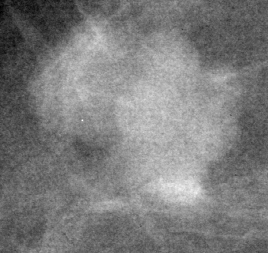
Crop from a digitized film mammogram around one marked abnormality; right breast; MLO view; BI-RADS breast density category 1 (scale 1–4).
Marked abnormality: mass, shape lobulated, margins circumscribed / ill defined; BI-RADS assessment category 4; pathology result (as recorded, not read from the image): benign.